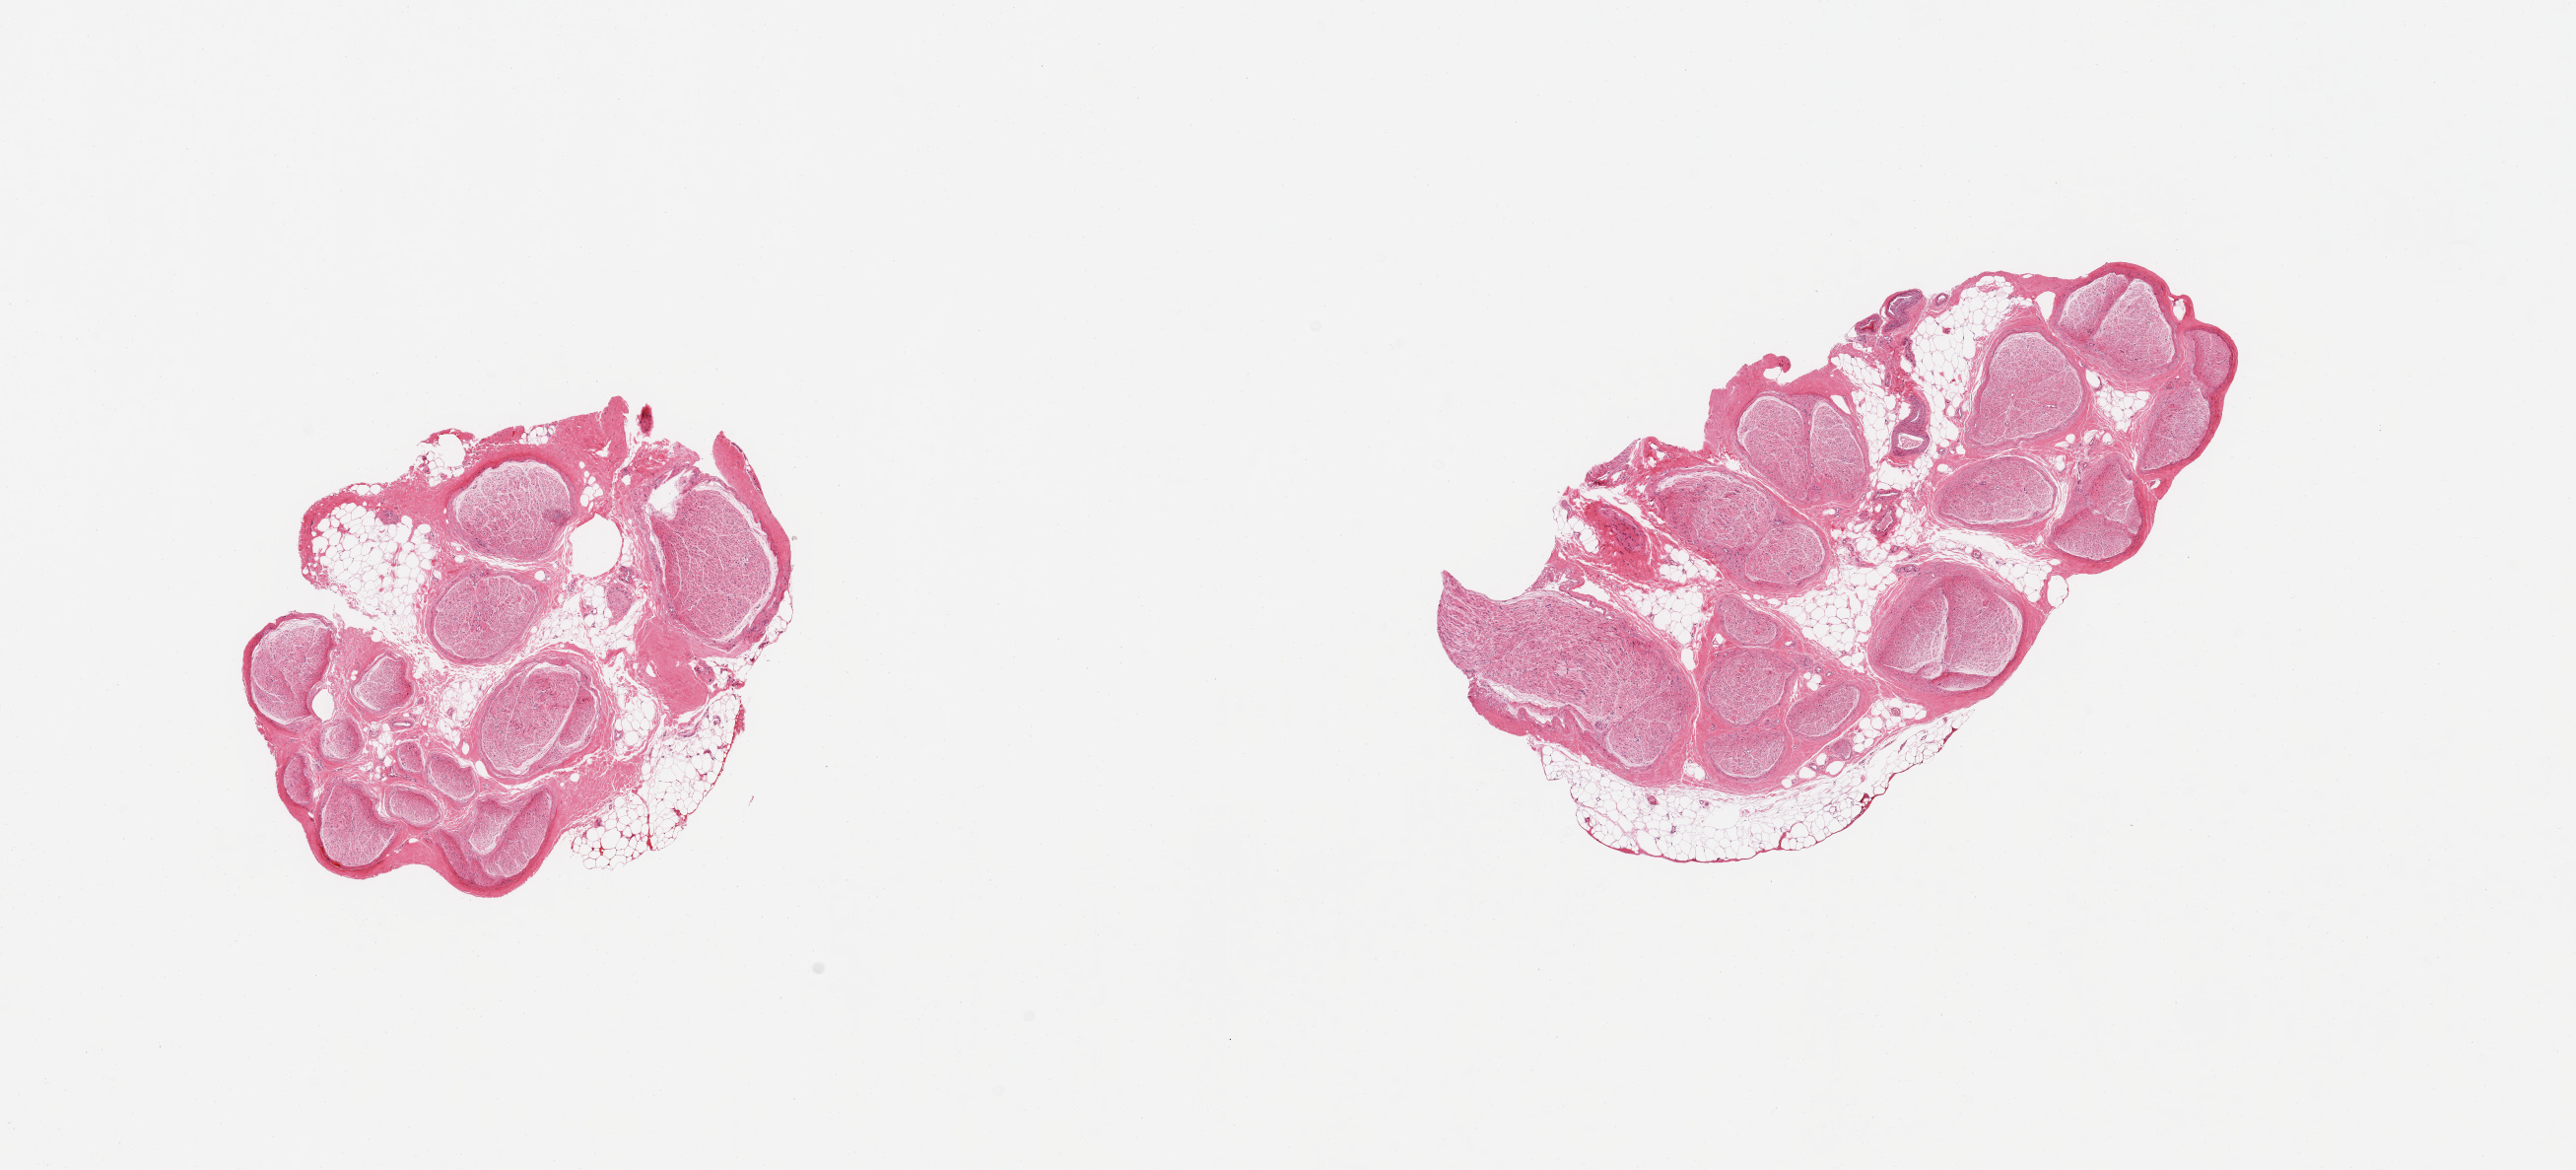
Digitized H&E-stained section, low-resolution overview of the scanned area, about 20.7 x 9.4 mm (from a 20x scan). PAXgene-fixed, paraffin-embedded tissue. Sampled site (target tissue): tibial nerve. Donor tissue sample.
- reviewer comment on this tissue sample: 2 pieces, trace nubbins of adherent fat up to ~0.5mm